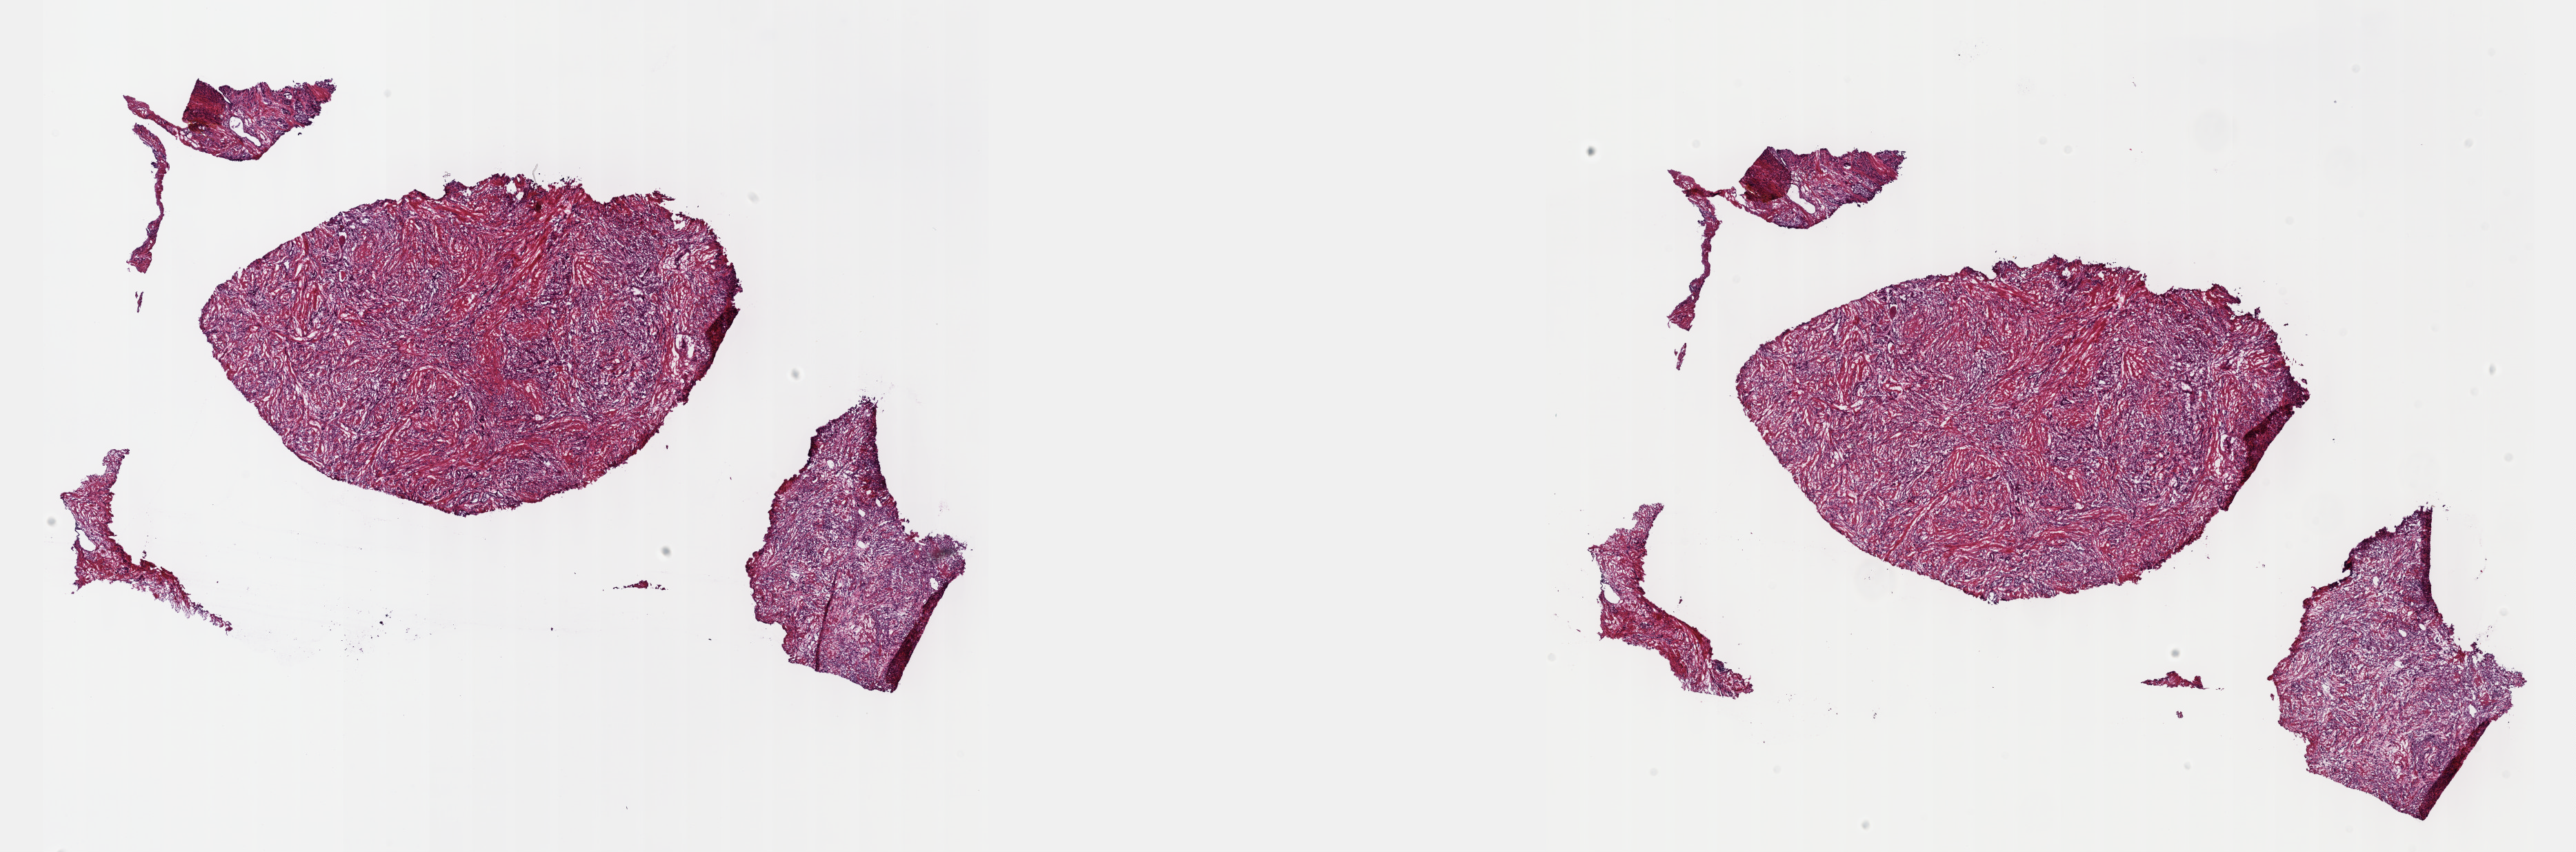
Whole-slide histology image, Hematoxylin and eosin (H&E) stained, whole scanned area (about 30.2 x 10.0 mm) shown as a low-resolution overview; frozen section from the top of the tissue portion; sample: primary tumour, prostate. Male, age 57 years at initial diagnosis. Gleason score: 9 (5+4). Pathologist review of this section (percent, as recorded): tumour cells 70%, tumour nuclei 70%, normal cells 0%, stromal cells 30%, necrosis 0%. Infiltration values recorded for this section: lymphocyte infiltration 5%, monocyte infiltration 0%, neutrophil infiltration 0%.
Pathologic diagnosis: Adenocarcinoma, NOS (prostate gland). Lymph nodes positive (case pathology): 6 of 10 examined.